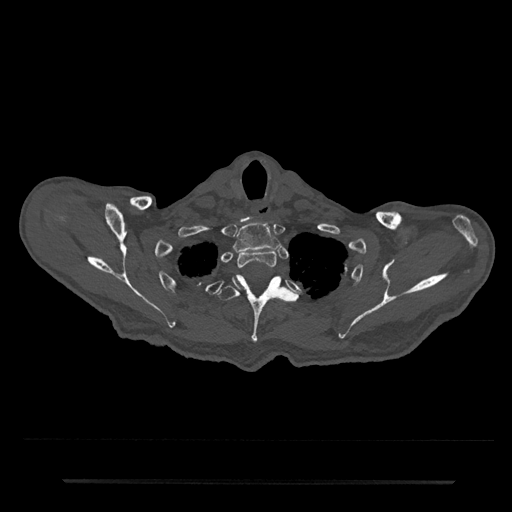
CT including the spine, one axial slice; position 683 of 797 along the scan axis; reconstruction kernel Br40s/3; bone window (W 1800 / L 400 HU); 0.5 mm slice thickness; 512 × 512 image matrix. Patient: male, 74 years. Case-level facts recorded for this patient, not image findings: primary cancer: prostate.
Annotated regions visible in this slice (semi-automatically segmented with operator editing):
- T1 vertebra: bounding box [x1, y1, x2, y2] px = [233, 223, 281, 253]
- T2 vertebra: [233, 250, 277, 286]
- T3 vertebra: [217, 274, 297, 343]